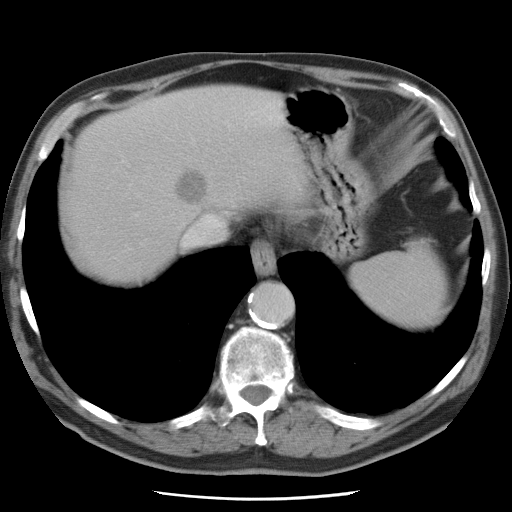
Contrast-enhanced abdominal CT, one axial slice. Slice 67 of 78 in the series (ordered by position). 120 kVp. Intravenous contrast given. Soft-tissue window (W 400 / L 40 HU). 5 mm slice thickness. 512 × 512 image matrix, field of view 337 × 337 mm. Male patient, age 75 years. Case-level facts recorded for this patient, not image findings: diagnosis: colorectal cancer liver metastases, imaged before liver resection; multiple liver metastases: yes; largest metastasis: 2.4 cm.
Outlined on this slice (manually delineated by an expert):
- hepatic veins: bounding box [x1, y1, x2, y2] px = [183, 125, 232, 246]
- liver: [69, 88, 300, 280]
- planned liver remnant (the part of the liver to remain after resection): [69, 144, 178, 282]
- liver metastasis: [175, 170, 209, 206]